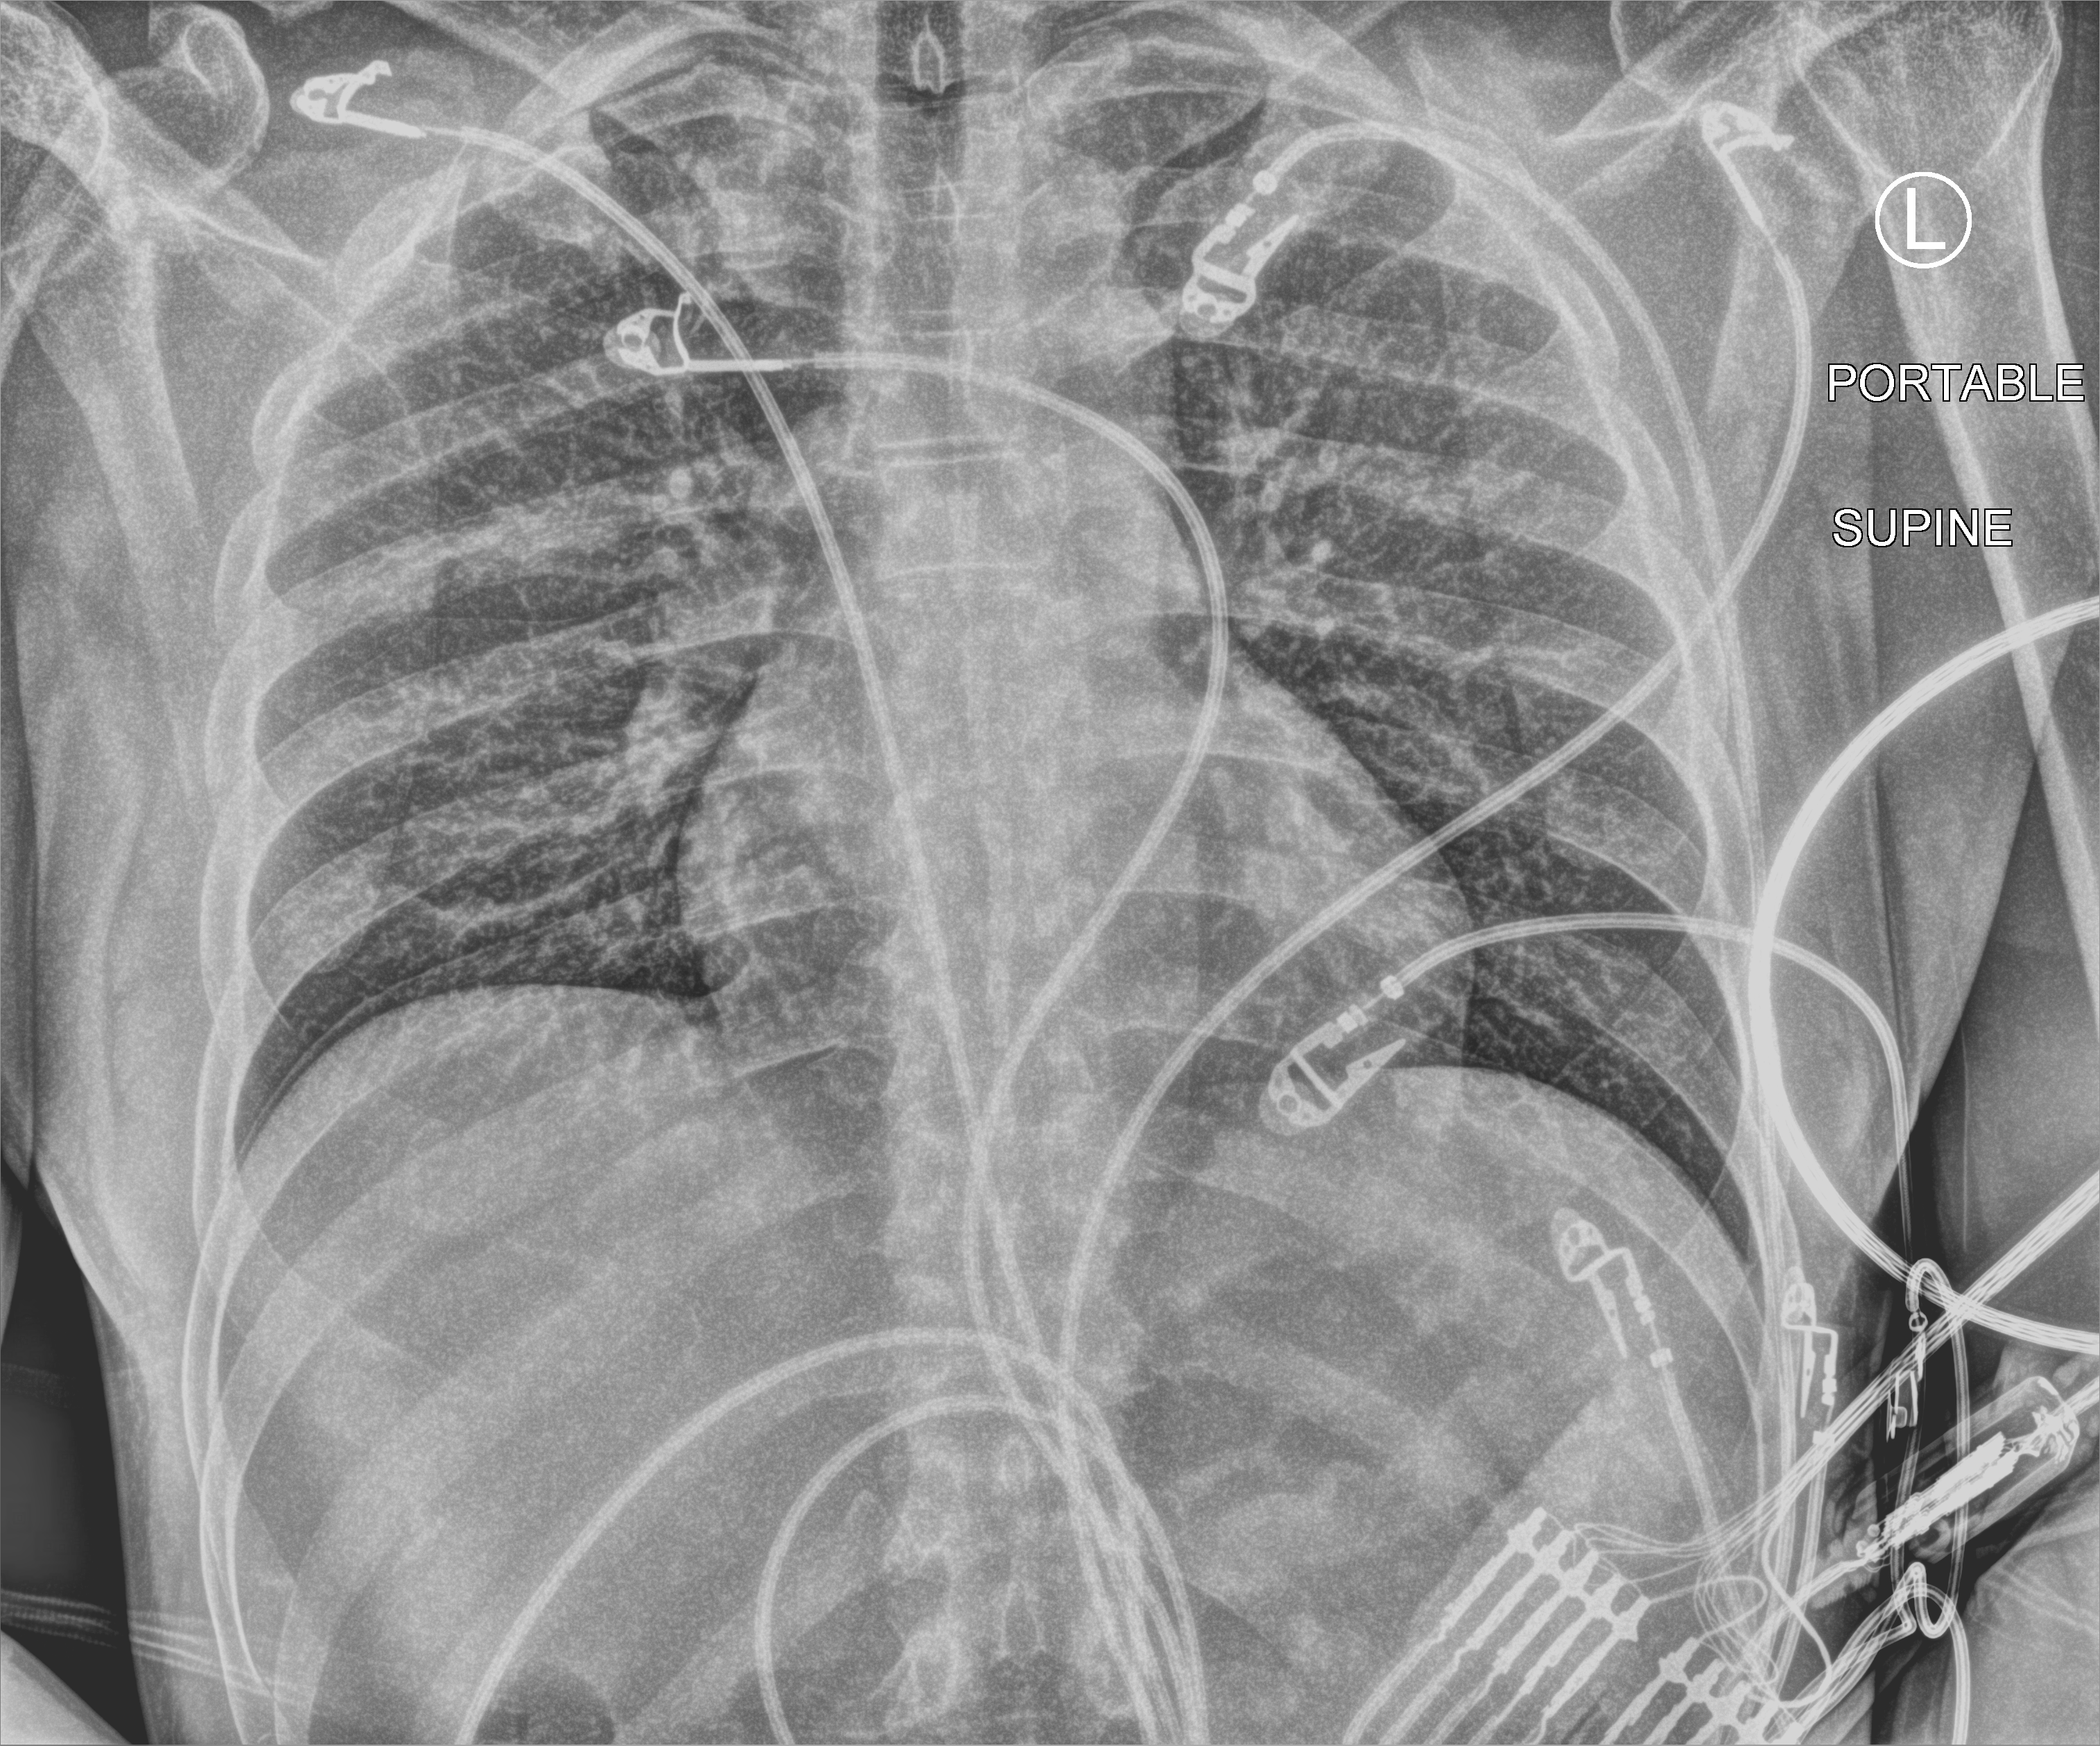
Bedside chest radiograph (computed radiography); anteroposterior (AP) projection. Male patient hospitalised with COVID-19, age 18–59 years.
Admission-level facts for this patient (not findings on this image; timing relative to this image not recorded): hypertension (admission record): no; other chronic lung disease (admission record): no; length of hospital stay: 3 days.